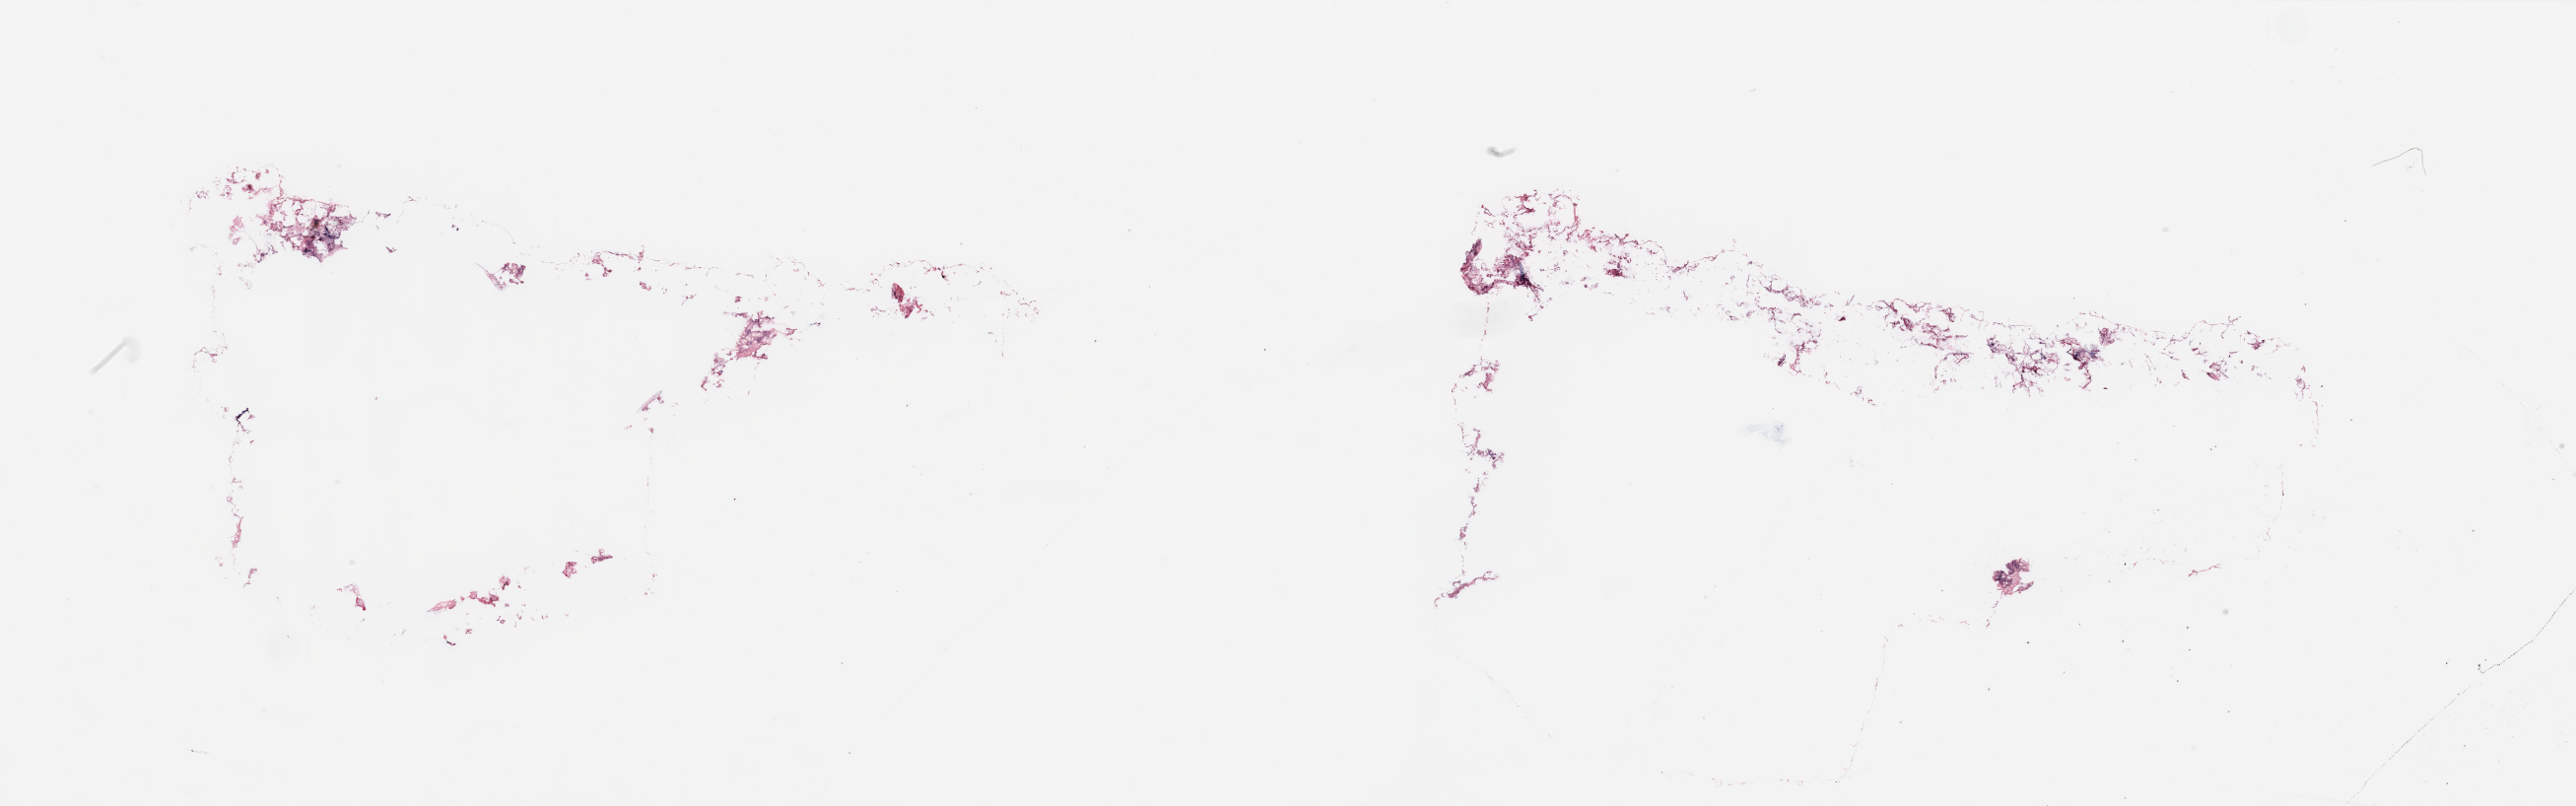
Whole-slide histology image, Hematoxylin and eosin (H&E) stained — low-resolution overview of the scanned area, about 41.3 x 12.9 mm (from a 20x scan). Breast, tissue type not recorded. Female, 60 y/o.
Patient diagnosis: Infiltrating duct carcinoma, NOS.